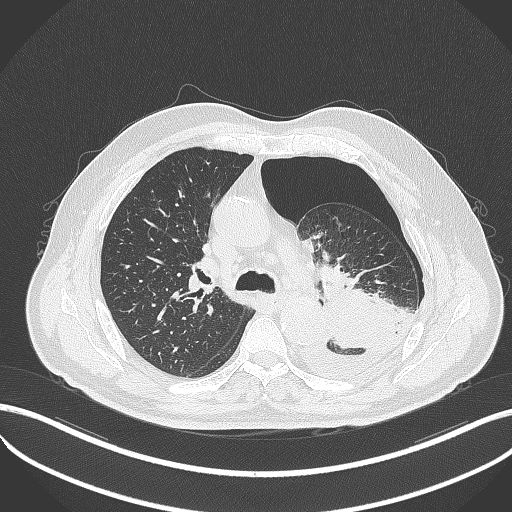
Chest CT, one axial slice. Position 339 of 464 along the scan axis. Reconstruction kernel B70f. Lung window (W 1500 / L -600 HU). 1 mm slice thickness. 512 × 512 image matrix. Male patient, age 76 years. From the clinical record (not read from this slice): clinical TNM (as recorded): T3 N0 M1b.
Annotated regions visible in this slice (bounding box drawn by a radiologist):
- lung tumour (recorded histology: adenocarcinoma): box from (x=315, y=274) to (x=398, y=350) px